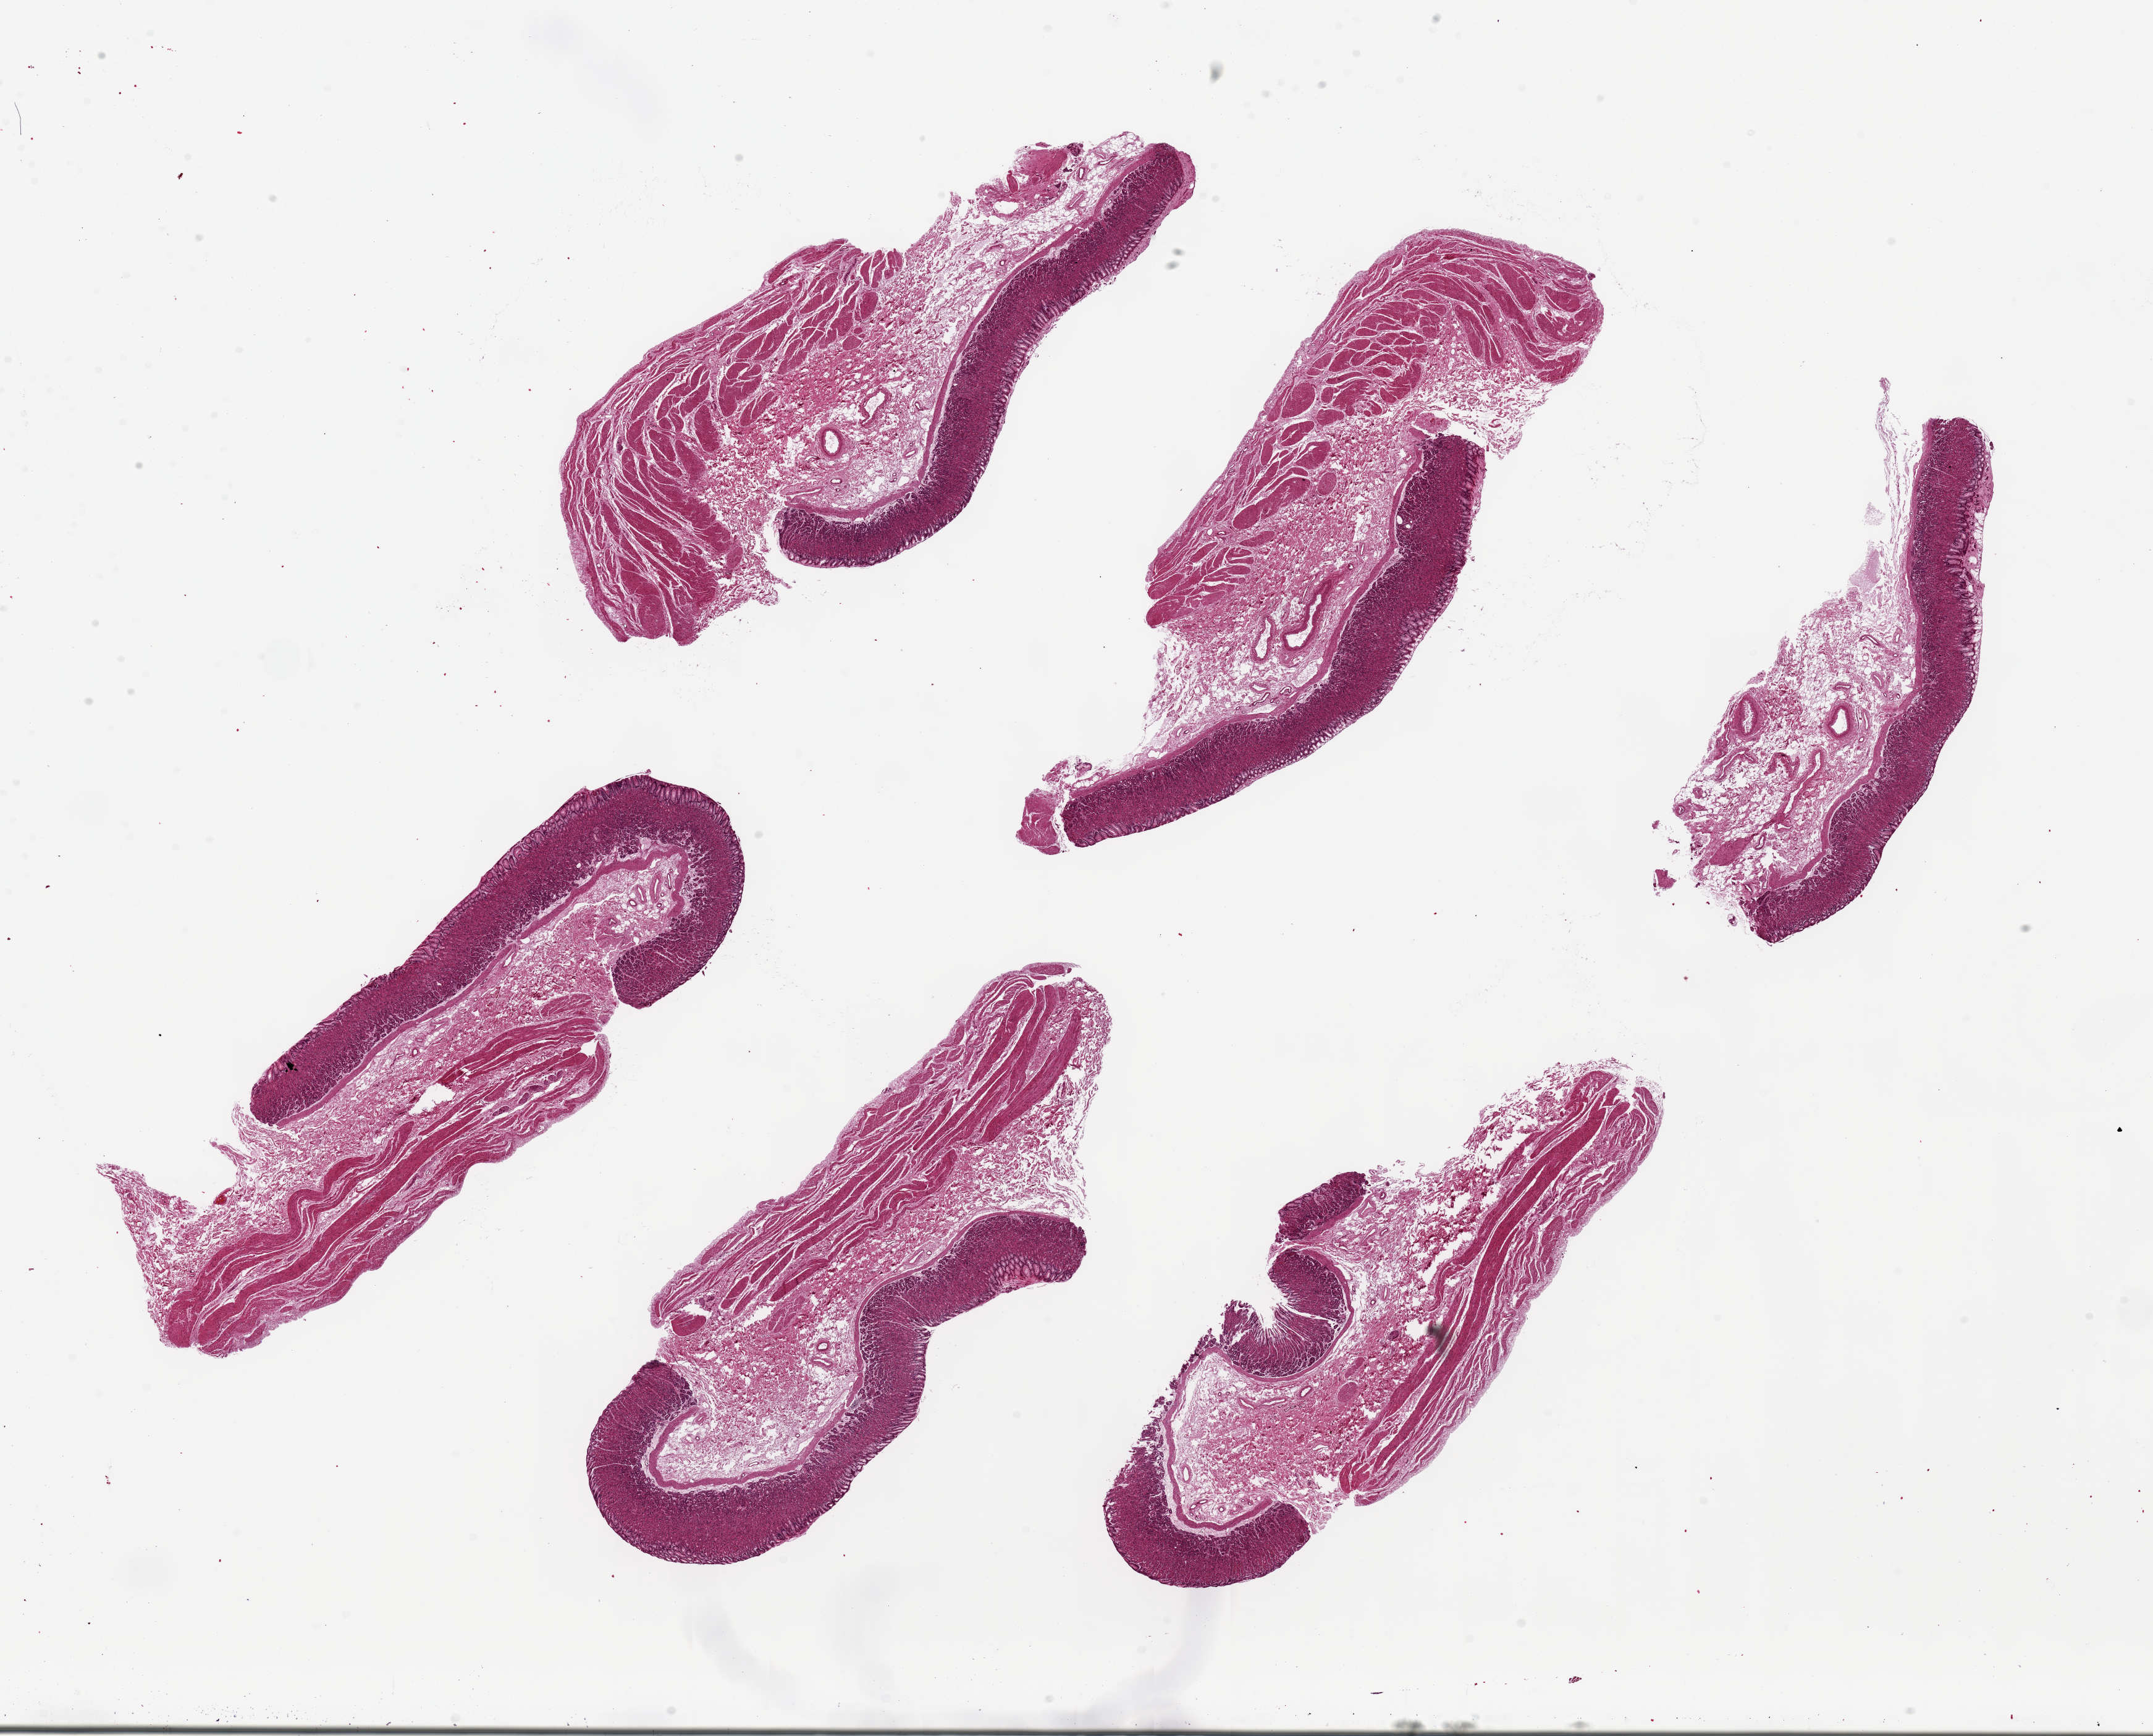
Digitized hematoxylin and eosin (H&E)-stained section, brightfield — whole scanned area (about 27.6 x 22.2 mm) shown as a low-resolution overview; PAXgene-fixed, paraffin-embedded tissue; sampled site (target tissue): stomach; donor tissue sample.
* reviewer comment on this tissue sample: 6 pieces up to 9.7x3.4 mm; excellent fundic mucosa